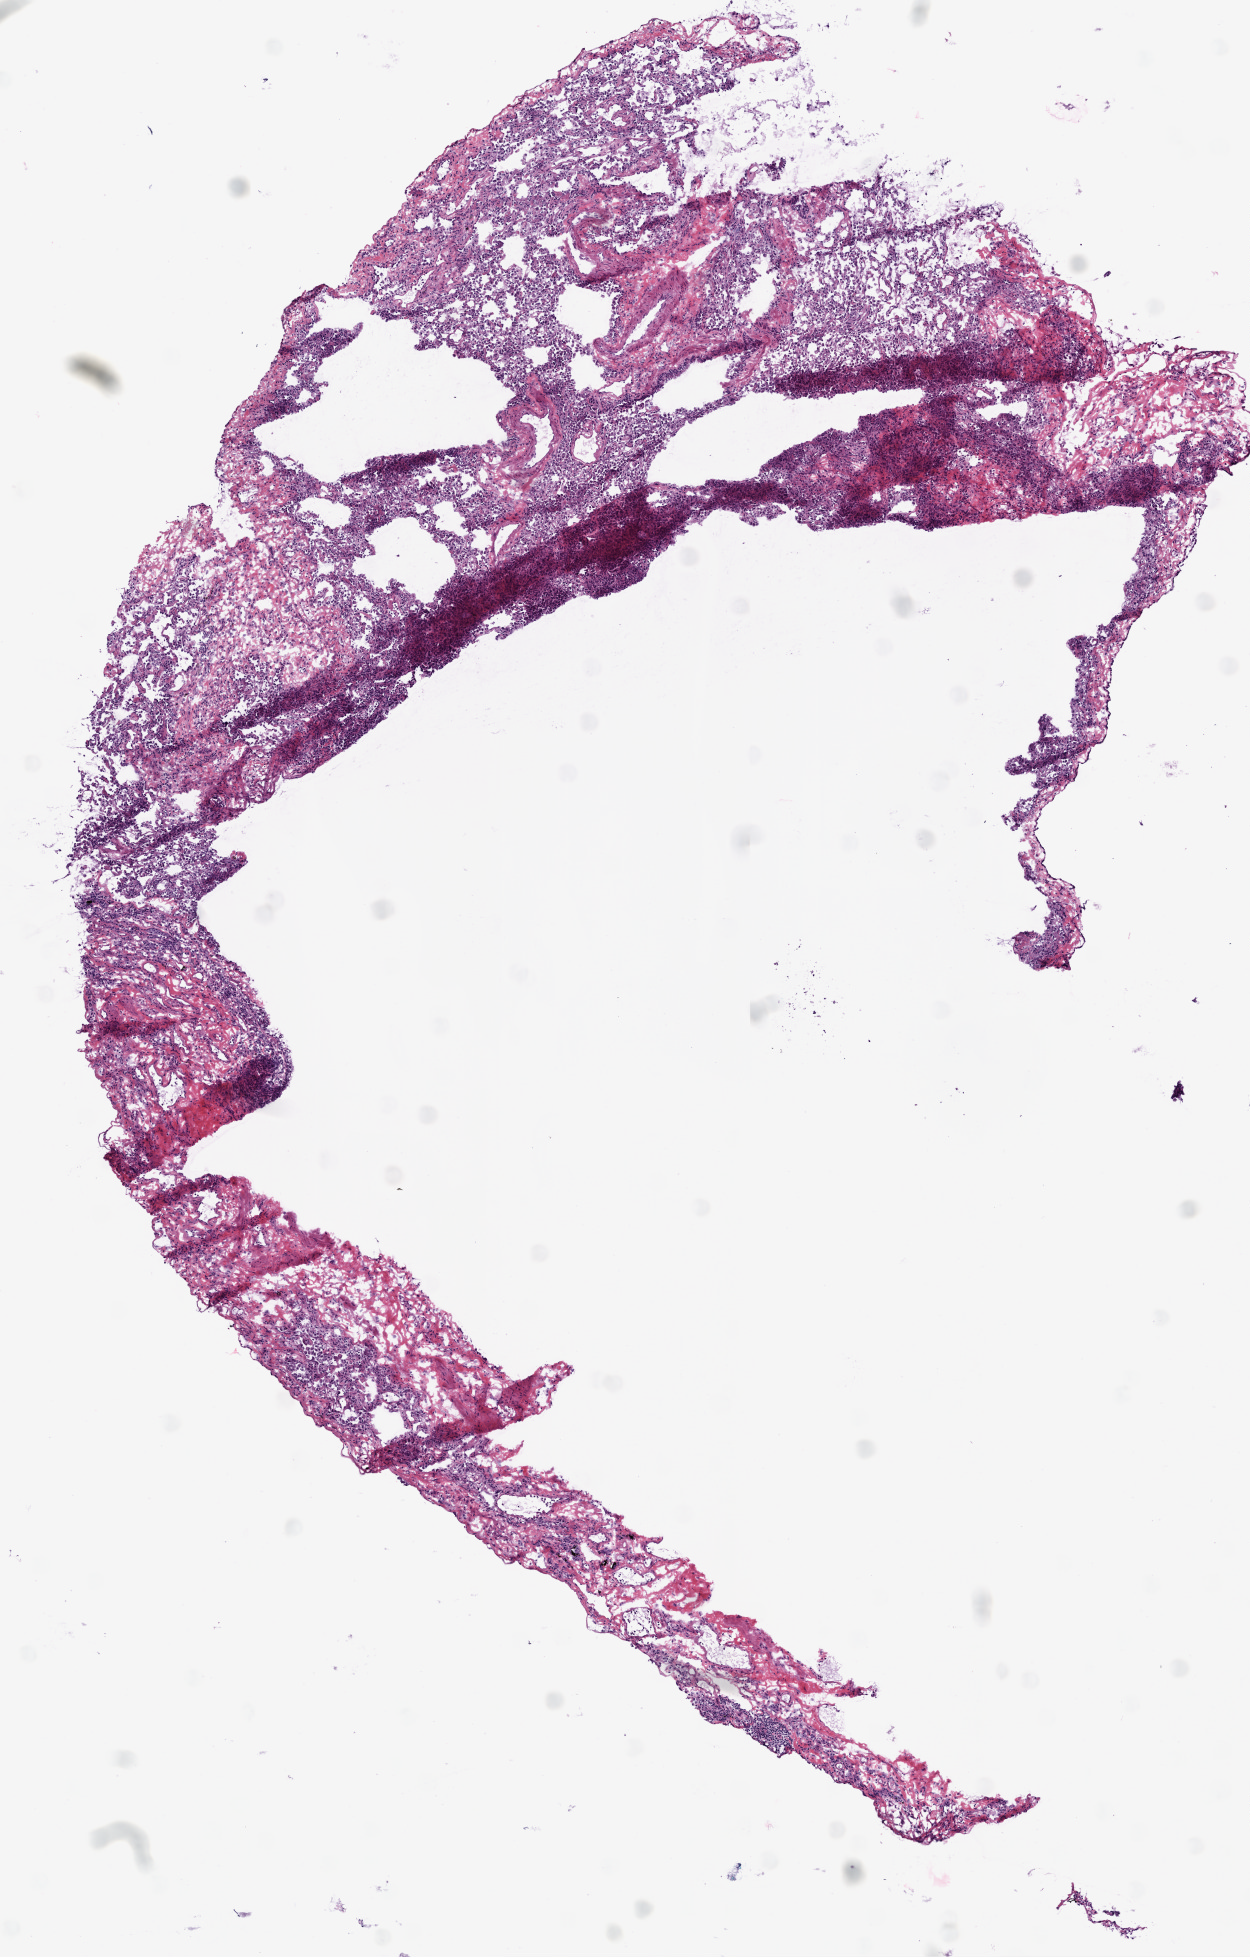
Whole-slide histology image, H&E — a low-resolution overview of the entire scanned area, about 5.0 x 7.9 mm (acquisition: 20x scan). Frozen section. Solid tissue normal (non-tumour tissue) sample from the lung. Male, age 72 years at initial diagnosis.
This section: solid tissue normal sample (biorepository sample class). Patient diagnosis: Squamous cell carcinoma, NOS (upper lobe, lung).